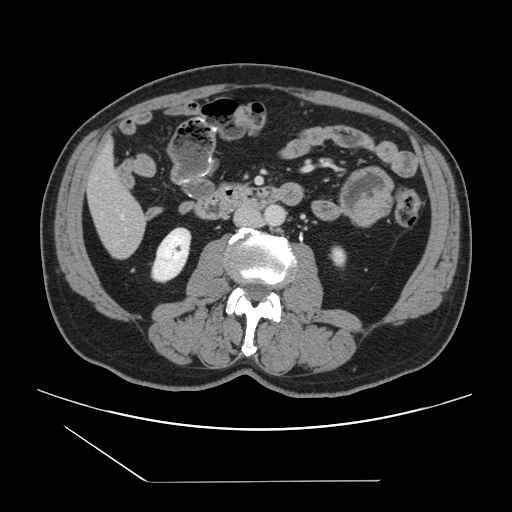
Contrast-enhanced abdominal CT, one axial slice; slice 30 of 157 in the series (ordered by position); 120 kVp; soft-tissue window (W 400 / L 40 HU); 2.5 mm slice thickness; 512 × 512 image matrix. Male patient, age 61 years. From the clinical record (not read from this slice): diagnosis: colorectal cancer liver metastases, imaged before liver resection; multiple liver metastases: yes; largest metastasis: 5.5 cm; disease in both lobes: yes.
Annotated regions visible in this slice (outlined manually by an expert reader):
- hepatic veins: box from (x=121, y=215) to (x=124, y=218) px
- liver: (x=88, y=149)–(x=146, y=258)
- planned liver remnant (the part of the liver to remain after resection): (x=87, y=148)–(x=142, y=219)